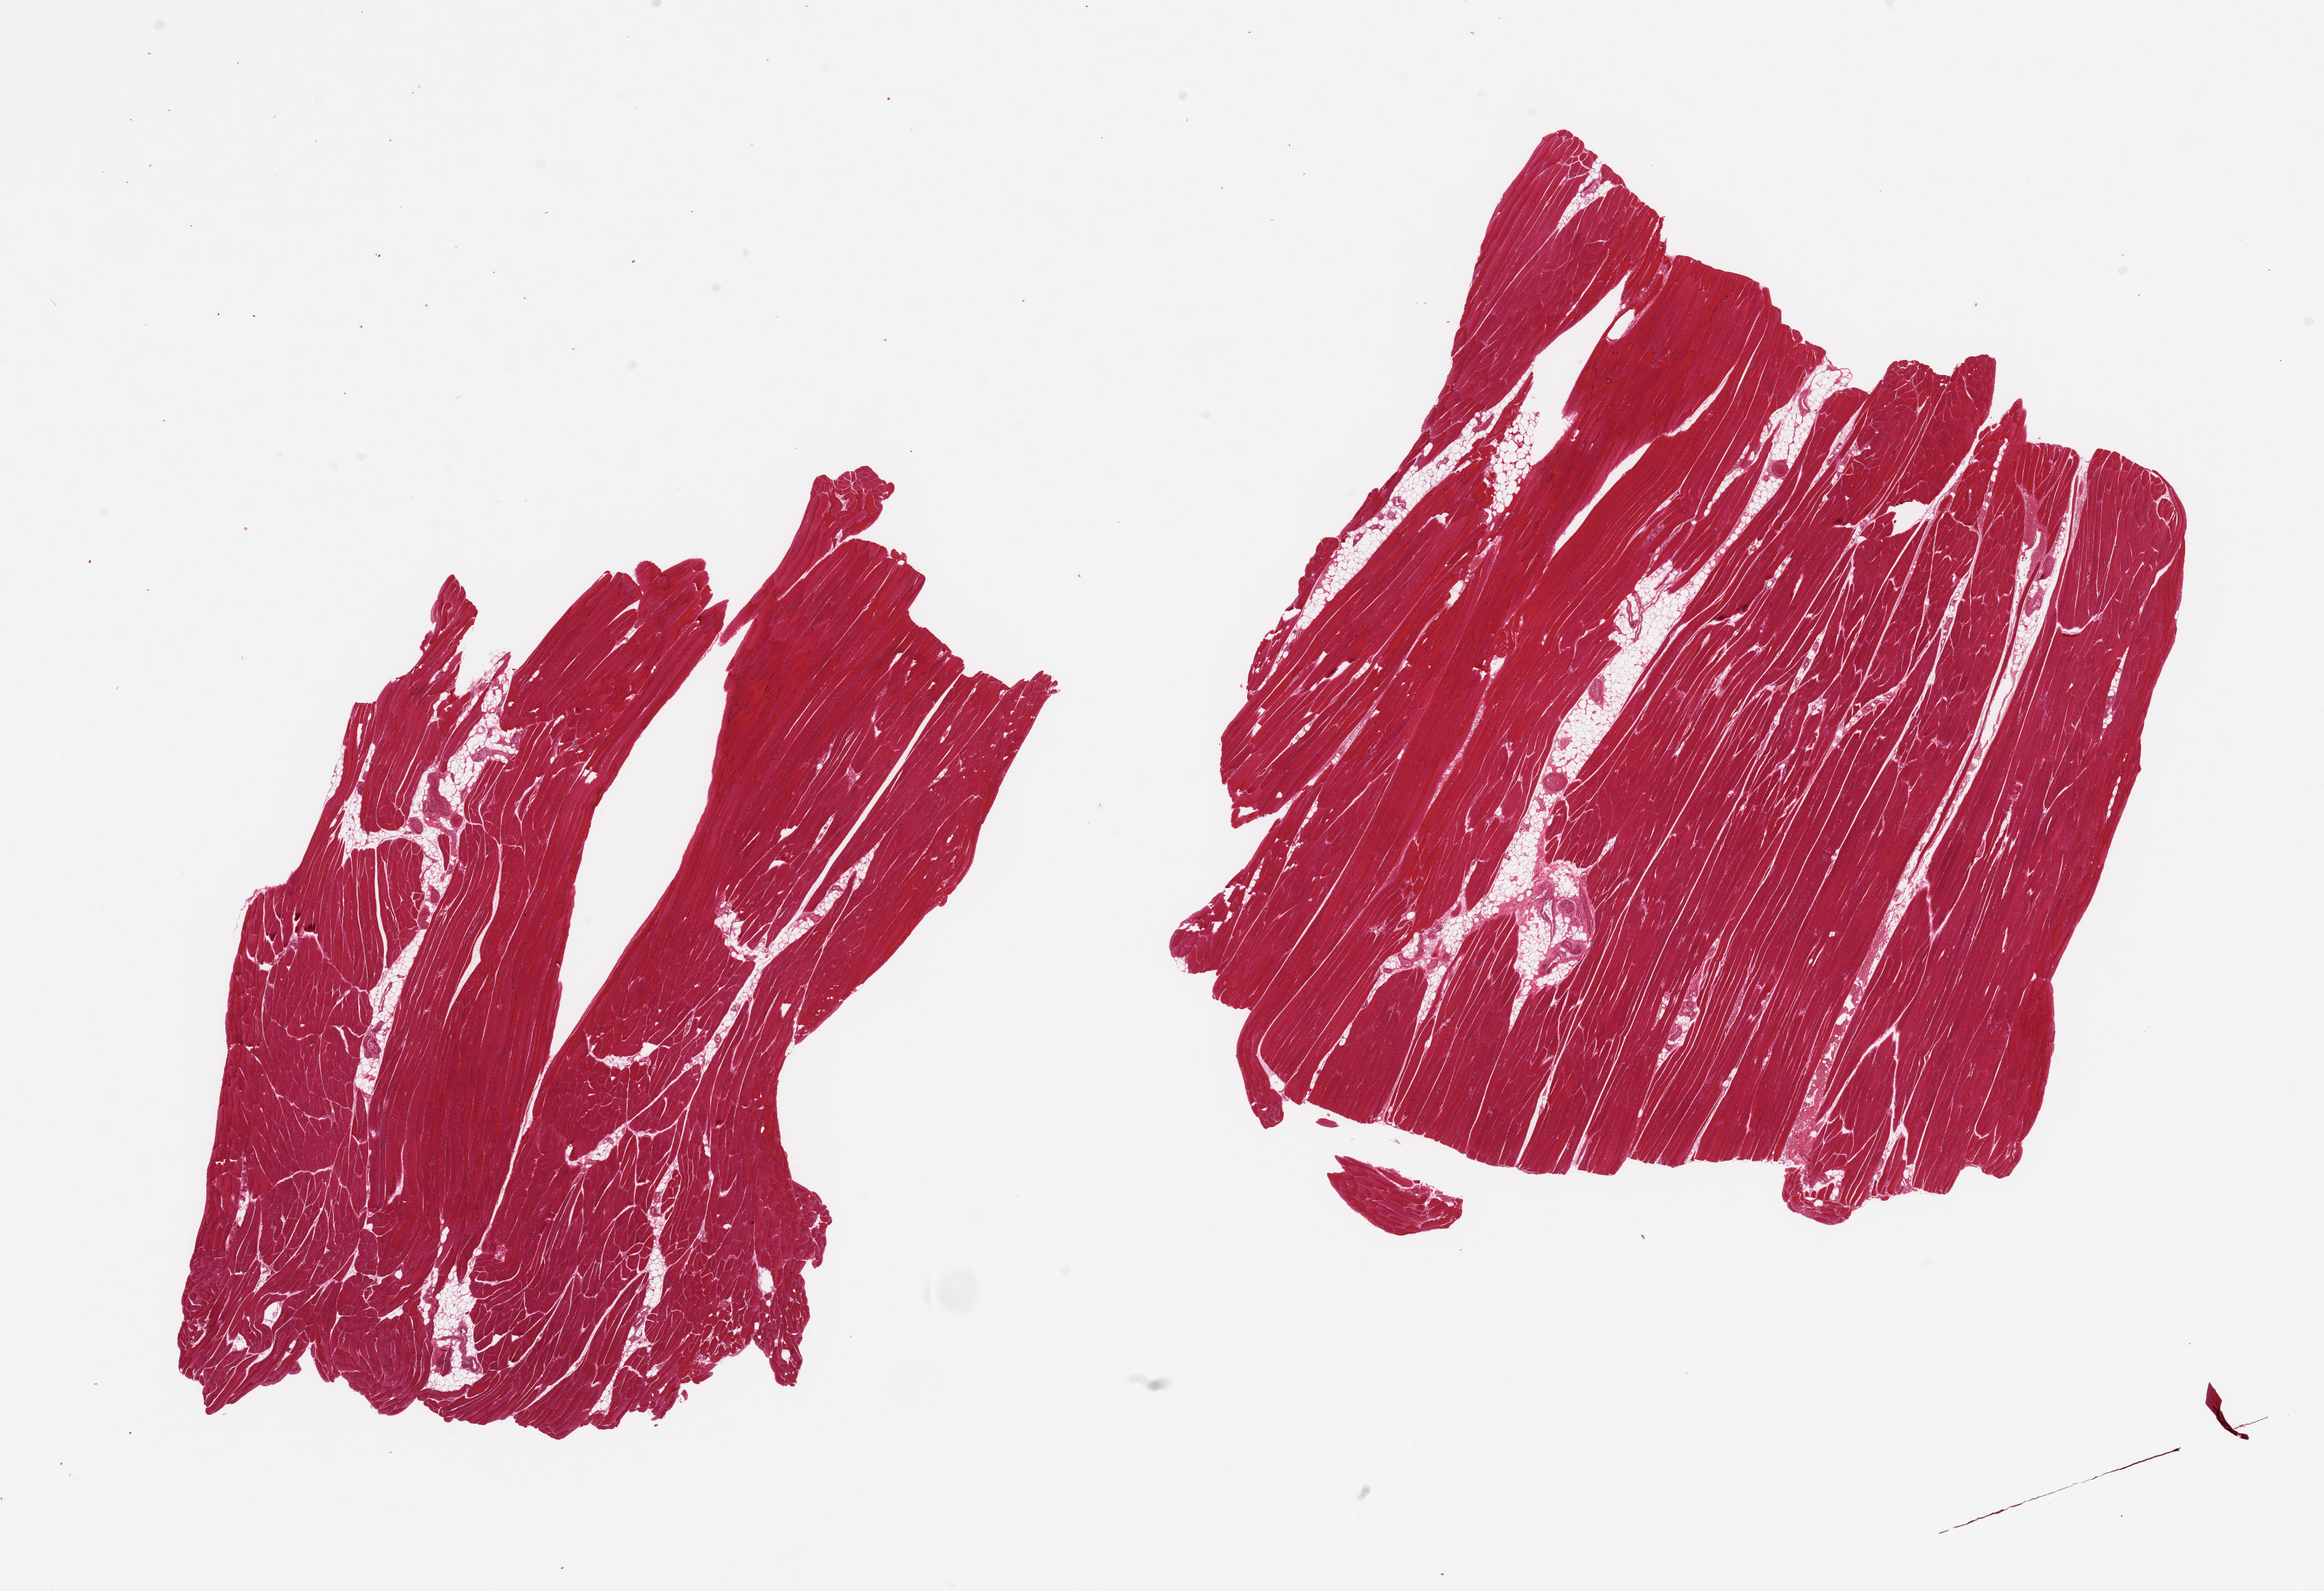
Haematoxylin and eosin whole-slide image, low-resolution overview of the scanned area, about 24.6 x 16.8 mm; PAXgene-fixed paraffin-embedded (PFPE) section; target tissue: skeletal muscle; tissue donor sample. Donor sex: male.
Reviewer comment on this tissue sample: 2 pieces, ~10% interstitial fat.